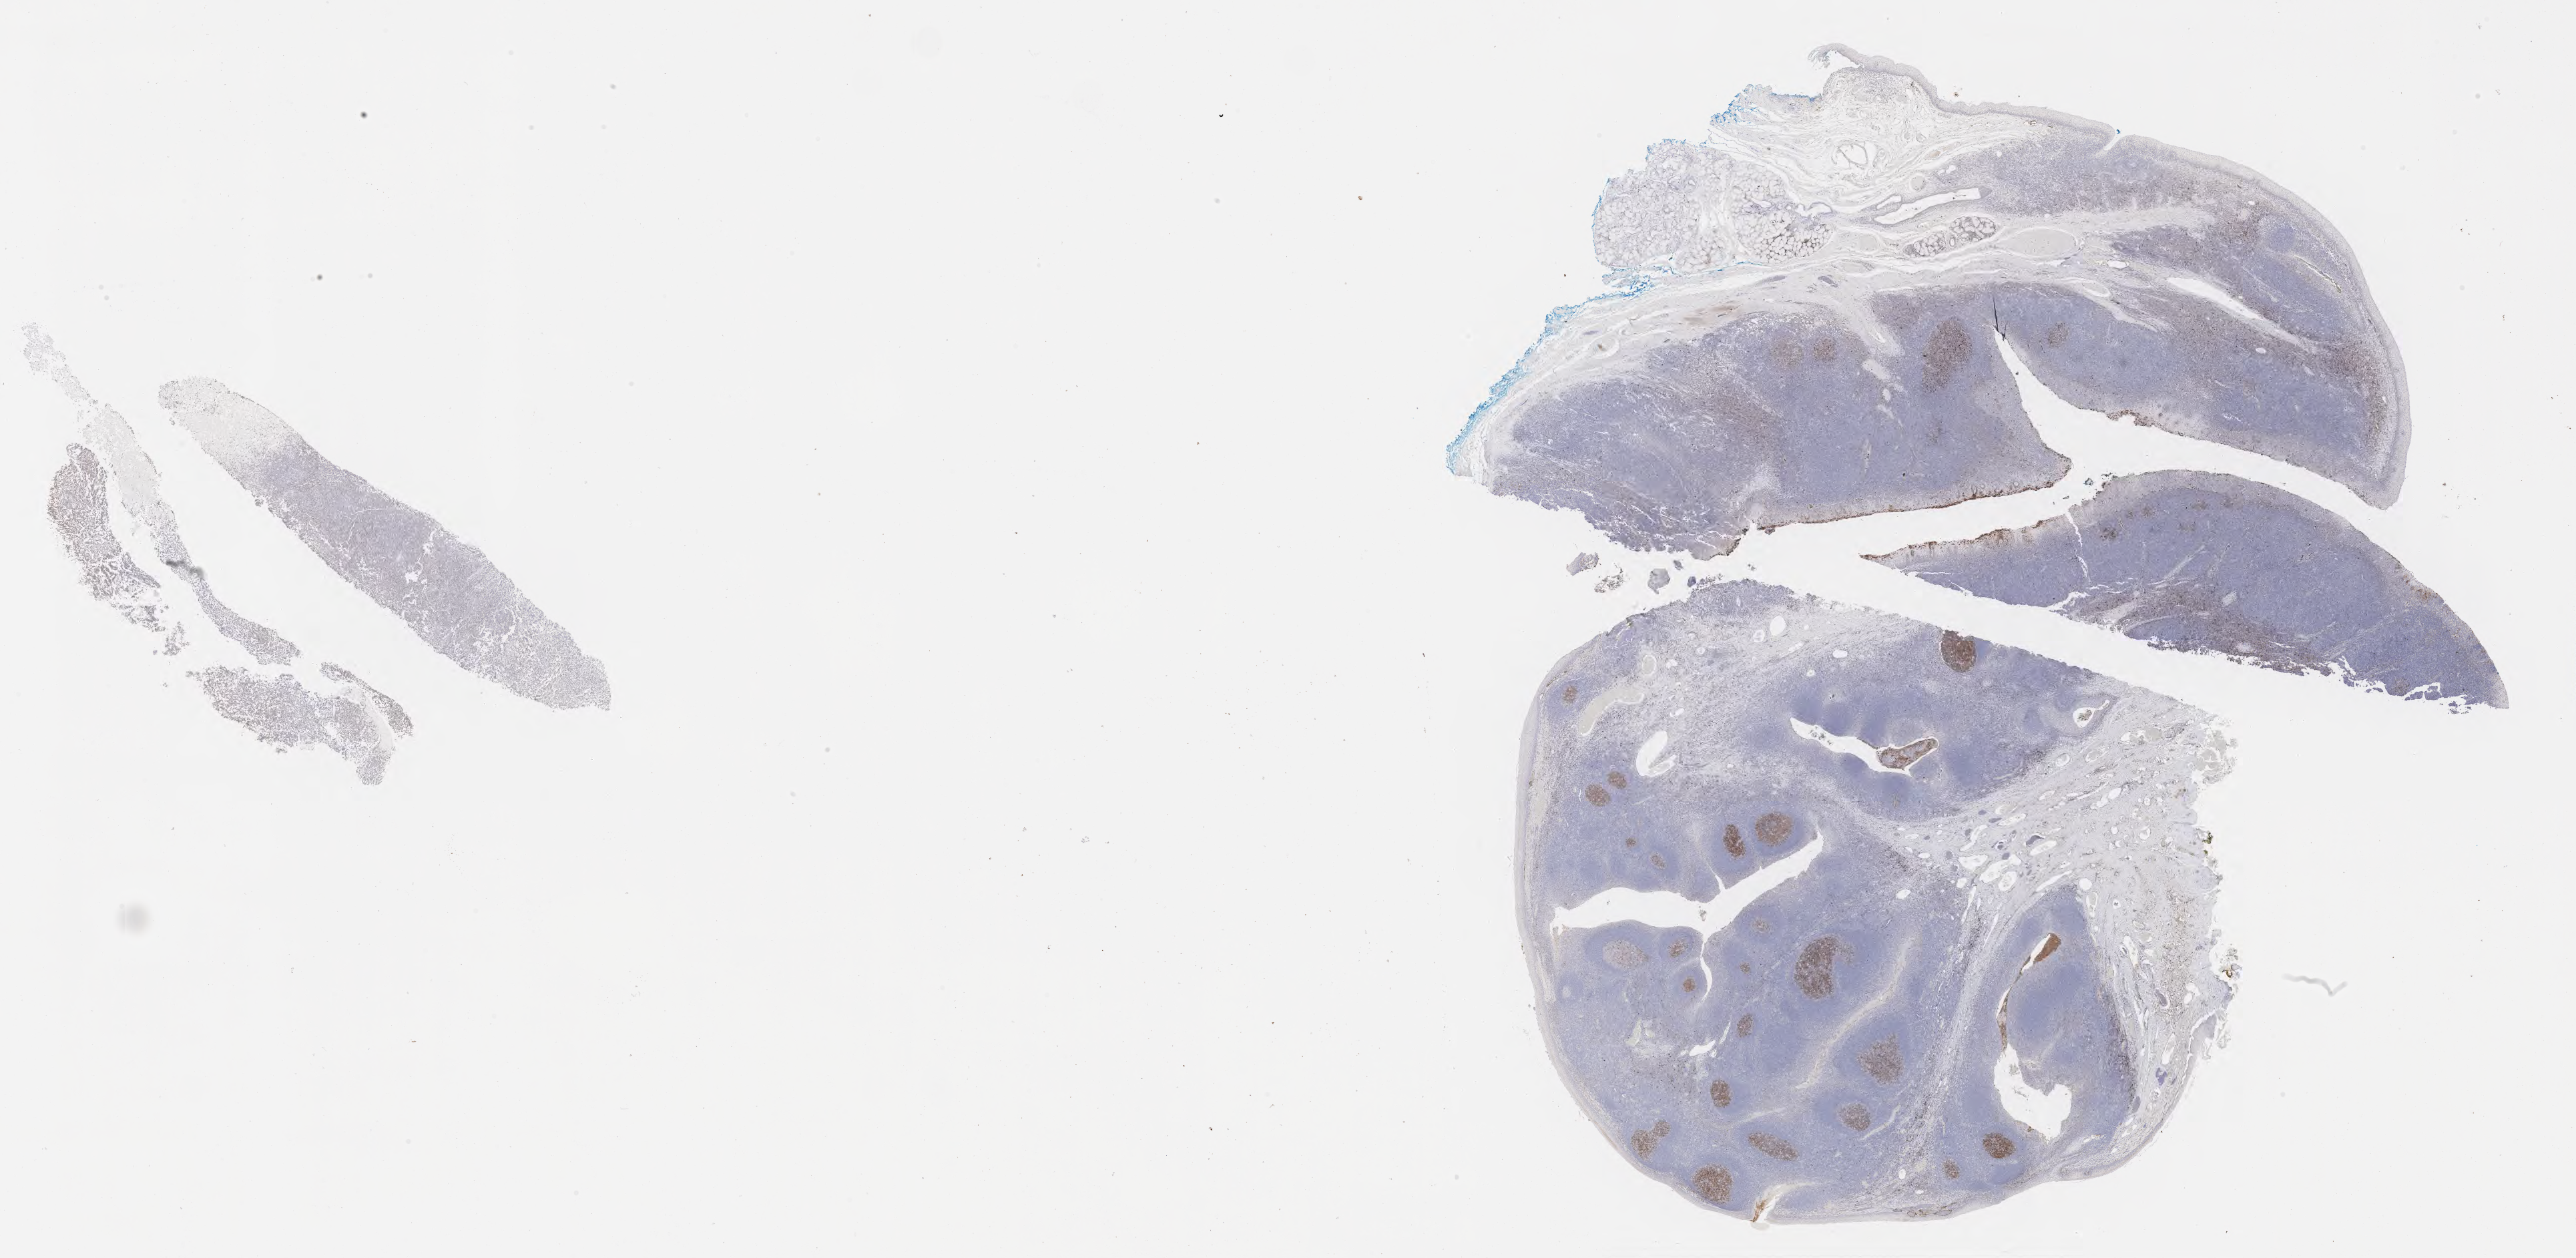
Immunohistochemistry (IHC) whole-slide image stained for CD10 — whole scanned area (about 31.2 x 15.2 mm) shown as a low-resolution overview, tumor tissue. Female patient, 18 years old.
Diagnosis: Burkitt lymphoma, NOS.